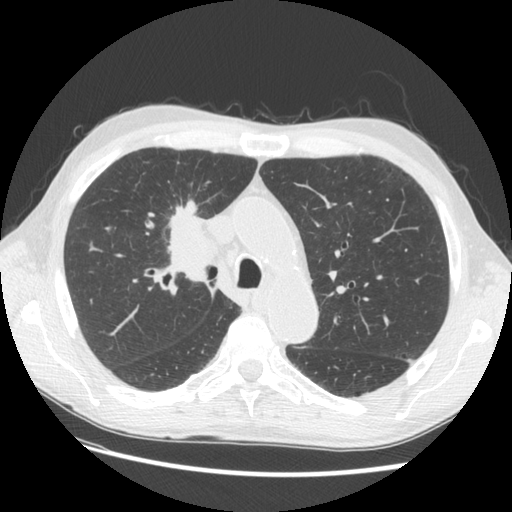
Chest CT (low-dose screening protocol), one axial image, third annual screen, lung window (W 1500 / L -600 HU), 2.5 mm slice thickness, 512 × 512 image matrix. Male, age 73 years at enrolment.
Lesion marked by an expert reader, bounding box (x1, y1, x2, y2) in pixels: (142, 184, 234, 277). The screening reader recorded 4 non-calcified nodules or masses ≥4 mm on this exam; which of them this box marks is not recorded. Participant outcome: lung cancer diagnosed 48 days after this screen — squamous cell carcinoma, NOS, right upper lobe, poorly differentiated (G3), stage IIIB (AJCC 6th edition), 56 mm at pathology.